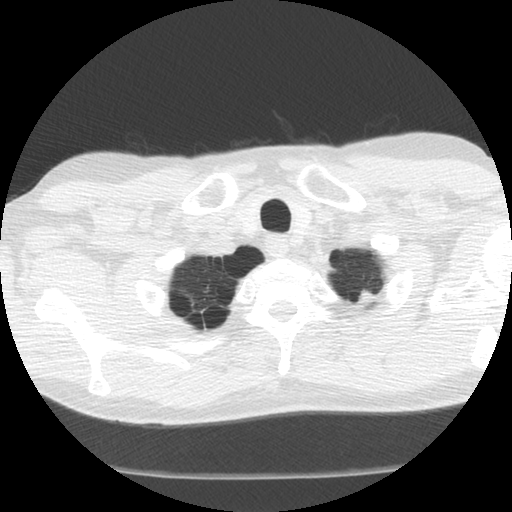
Axial slice from a low-dose chest CT screening exam. First (baseline) screen. Lung window (W 1500 / L -600 HU). 2.5 mm slice thickness. Slice 120 of 130 in the series. 512 × 512 image matrix, field of view 326 × 326 mm. Male, age 63 years at enrolment.
Expert reader's lesion annotation, bounding box [x1, y1, x2, y2] px = [343, 280, 387, 318]. The screening reader recorded 4 non-calcified nodules or masses ≥4 mm on this exam; which of them this box marks is not recorded. Official screen result: positive, change unspecified: nodule(s) >= 4 mm or enlarging nodule(s), mass(es), or other non-specific abnormalities suspicious for lung cancer. Lung cancer was diagnosed 629 days after this screen (after the second annual screen): adenocarcinoma, NOS, left upper lobe, moderately differentiated (G2), stage IB (AJCC 6th edition), 14 mm at pathology.